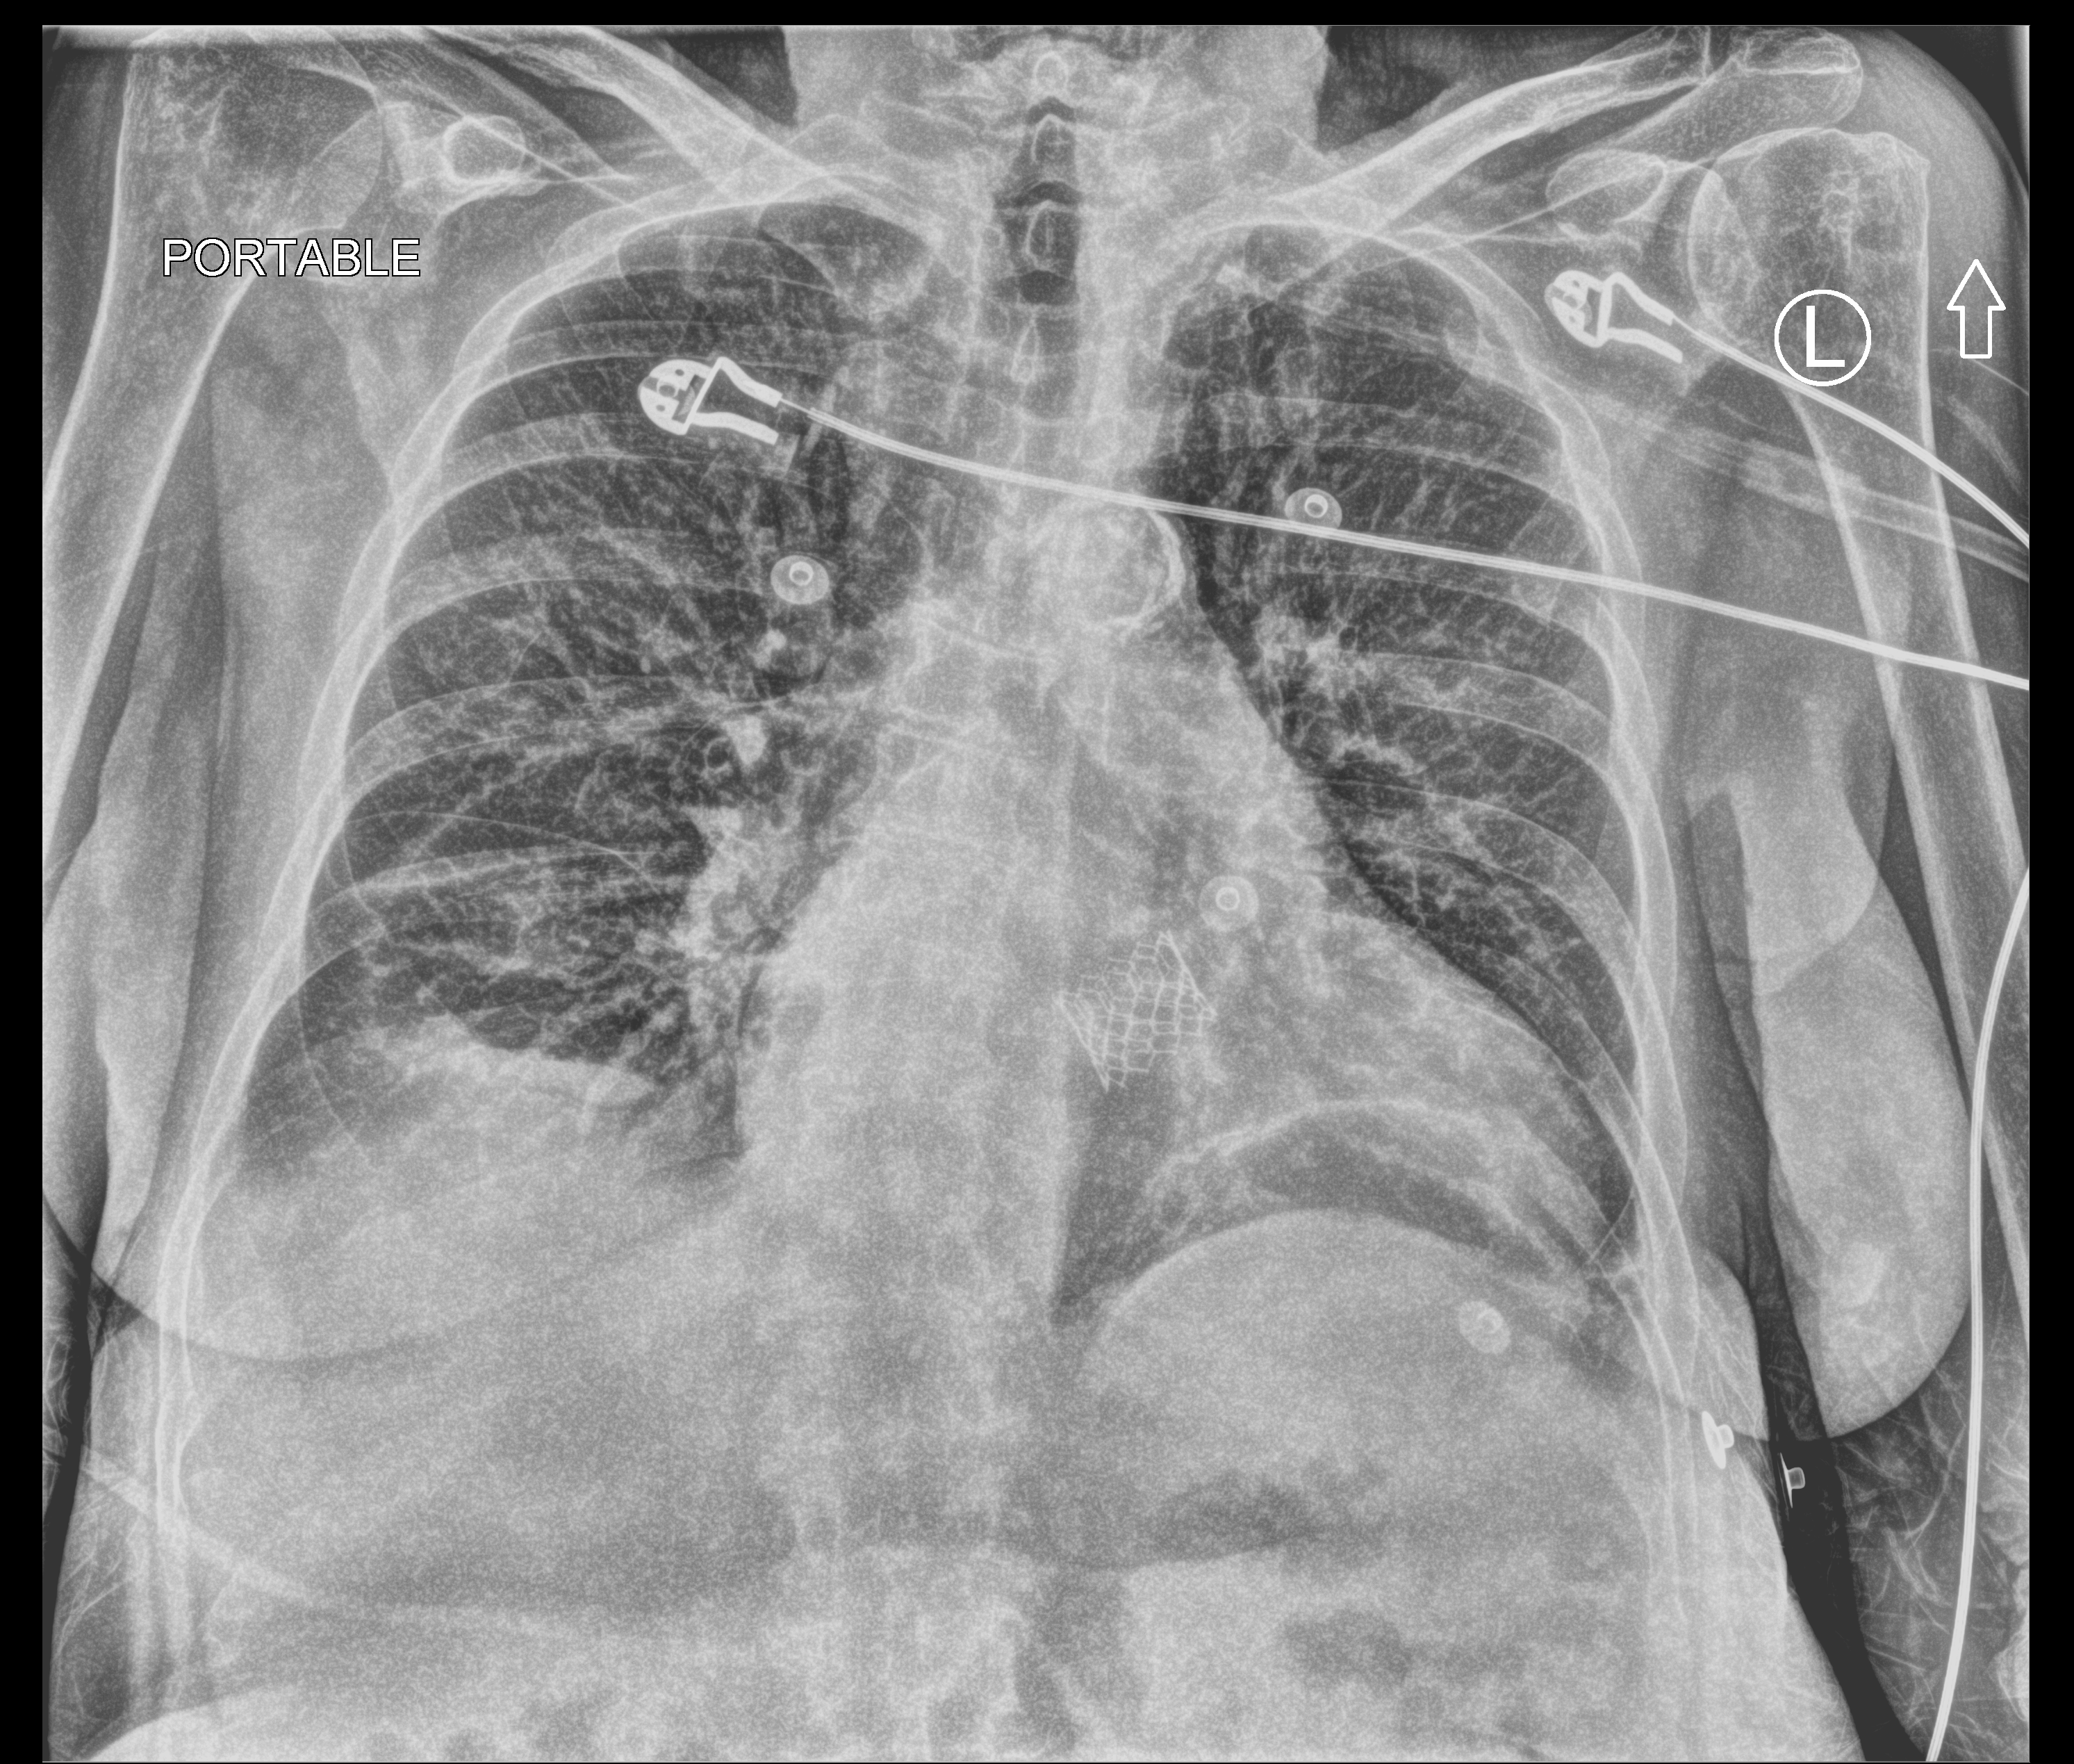
Portable chest radiograph; anteroposterior (AP) projection. Female patient hospitalised with COVID-19, age 75–90 years.
Admission-level facts for this patient (not findings on this image; timing relative to this image not recorded): mechanically ventilated during this hospital stay: no.